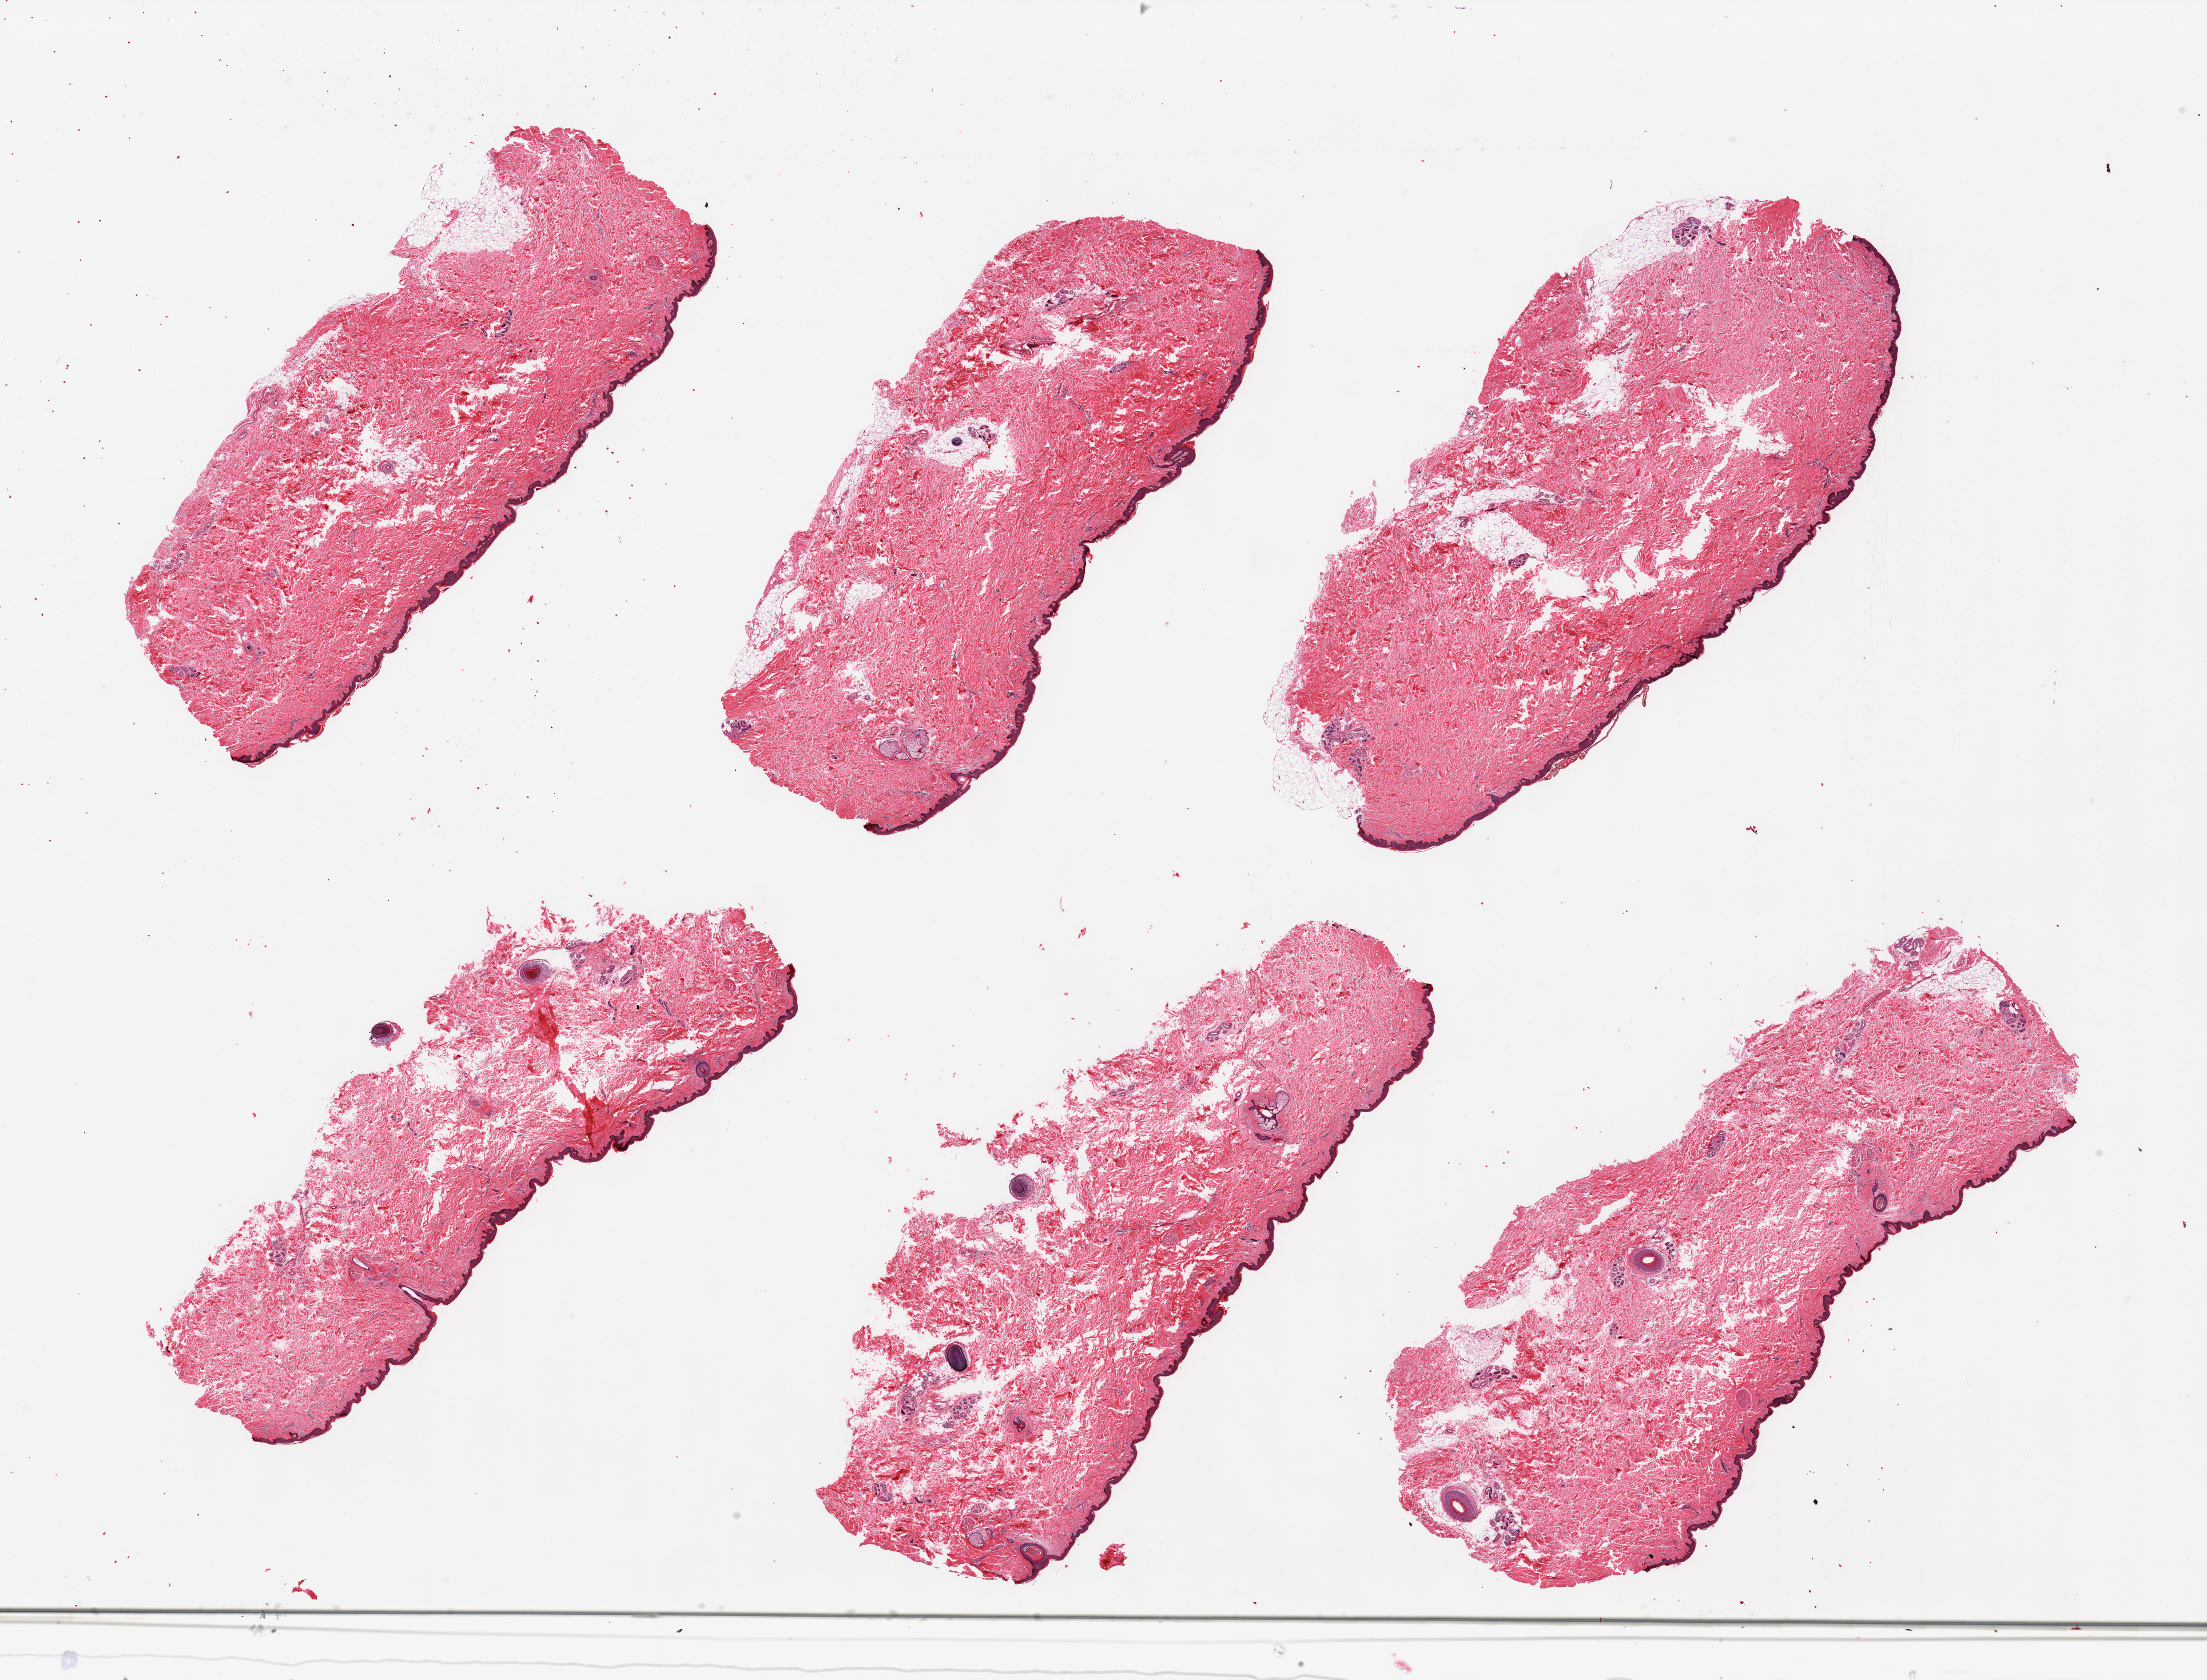
Whole-slide image, hematoxylin and eosin (H&E) stain — low-resolution overview of the scanned area, about 30.5 x 23.2 mm; PAXgene-fixed, paraffin-embedded tissue; target tissue: skin of suprapubic region; donor tissue sample. Donor sex: male.
- reviewer comment on this tissue sample: 6 pieces; predominantly well trimmed, but with up to ~10% internal and attached fat